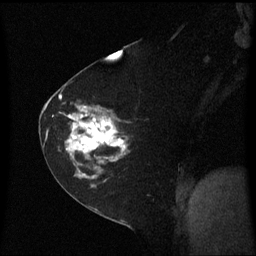
Breast MRI (dynamic contrast-enhanced), one sagittal slice. Position 38 of 60 along the scan axis. Dynamic contrast-enhanced series, image 2 of 3 at this slice position (ordered by acquisition). 1.5 T. TE 4.2 ms, TR 8.4 ms. 2 mm slice thickness. 256 × 256 image matrix. Female patient, age 60 years. From the clinical record (not read from this slice): setting: breast cancer imaged before/during neoadjuvant chemotherapy; receptor status: triple-negative.
Annotated regions visible in this slice (semi-automatically segmented with operator editing):
- analysis volume of interest (the breast-tissue region the enhancement analysis was run in; not a lesion): bounding box [x1, y1, x2, y2] px = [45, 99, 132, 182]
- tumour enhancement mask (voxels above the 70 % enhancement threshold inside the analysis volume of interest): [45, 99, 127, 180]